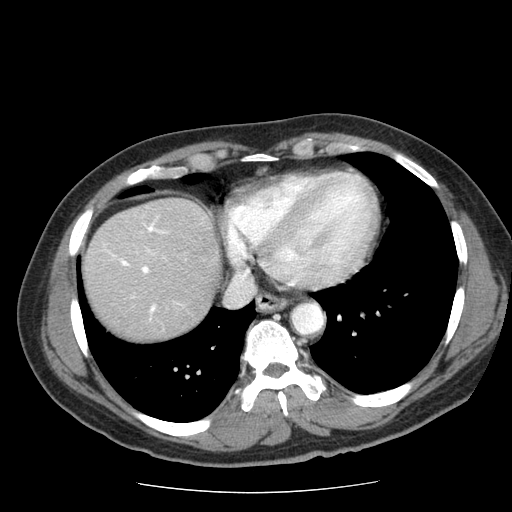
Contrast-enhanced abdominal CT (liver protocol), one axial slice. Slice 64 of 85 in the series (ordered by position). Reconstruction kernel STANDARD. Soft-tissue window (W 400 / L 40 HU). 512 × 512 image matrix. From the clinical record (not read from this slice): diagnosis: hepatocellular carcinoma (patient treated with transarterial chemoembolisation; whether this scan precedes or follows treatment is not stated here); TNM stage (as recorded): Stage-IIIA; Child-Pugh class: A; tumour differentiation: well differentiated; tumour nodularity: multinodular.
Annotated regions visible in this slice (semi-automatically segmented with operator editing):
- liver parenchyma outside the tumour (the mass and vessels are separate outlines, so this box may not span the whole liver): bounding box <84,198,220,340> (left, top, right, bottom; pixels)
- liver vessels: <112,219,166,321>